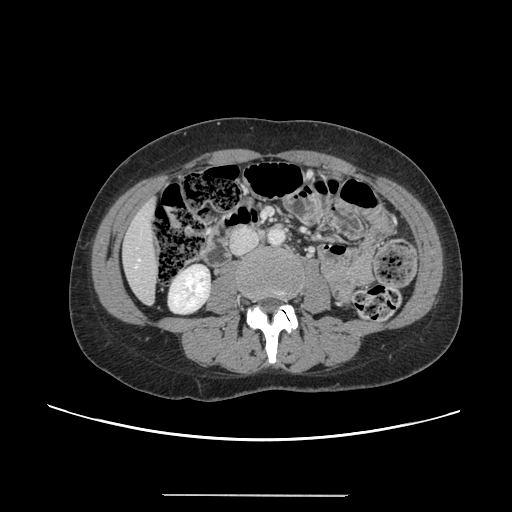
Contrast-enhanced abdominal CT, one axial slice; intravenous contrast given; soft-tissue window (W 400 / L 40 HU); 512 × 512 image matrix, field of view 380 × 380 mm. Female patient, age 53 years. From the clinical record (not read from this slice): diagnosis: colorectal cancer liver metastases, imaged before liver resection; multiple liver metastases: yes; largest metastasis: 1.1 cm; disease in both lobes: no.
Annotated regions visible in this slice (manually delineated by an expert):
- liver: bounding box (x1, y1, x2, y2) in pixels: (124, 204, 159, 302)
- planned liver remnant (the part of the liver to remain after resection): (124, 203, 159, 302)